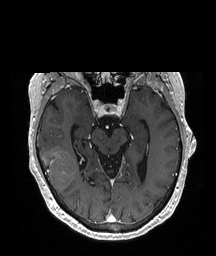
Brain MRI from a brain-tumour surgery series, one axial slice; position 127 of 208 along the scan axis; T1-weighted post-contrast; 1 mm slice thickness; 216 × 256 image matrix. Case-level facts recorded for this patient, not image findings: histopathology: Glioblastoma; WHO grade: 4; IDH mutation: no.
Outlined on this slice (outlined manually by an expert reader):
- tumour: bounding box <42,151,76,193> (left, top, right, bottom; pixels)